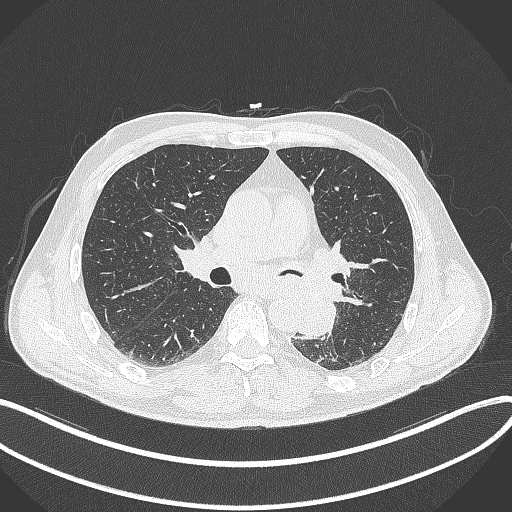
Chest CT, one axial slice. Position 197 of 329 along the scan axis. Reconstruction kernel B70f. 120 kVp. Lung window (W 1500 / L -600 HU). 1 mm slice thickness. 512 × 512 image matrix. Male patient, age 59 years. From the clinical record (not read from this slice): clinical TNM (as recorded): T2a N2 M0.
Annotated regions visible in this slice (rectangle marked by the reading radiologist):
- lung tumour (recorded histology: squamous cell carcinoma): bounding box <291,289,339,339> (left, top, right, bottom; pixels)